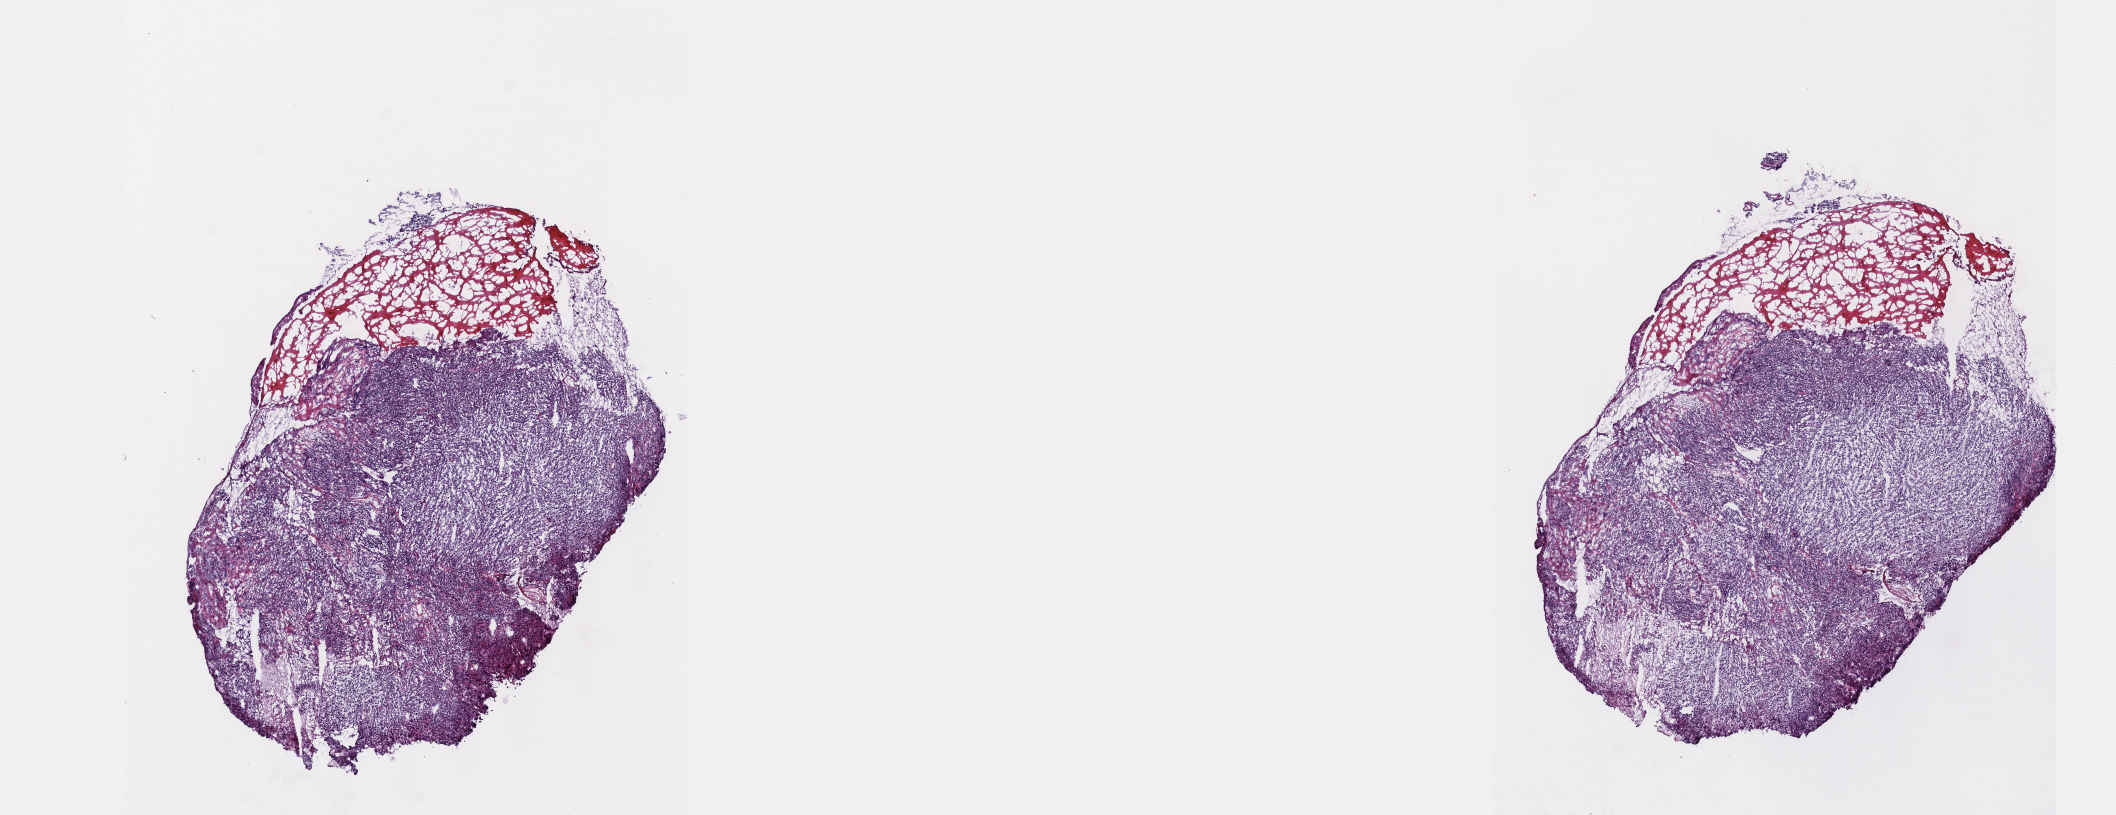
Digitized H&E tissue section (whole slide) — whole scanned area (about 17.1 x 6.6 mm) shown as a low-resolution overview, frozen section from the top of the tissue portion, cervix, primary tumour sample. Patient: female, age at initial diagnosis 72 years. Histologic grade: G3 (poorly differentiated). Composition of this section per pathologist review: tumour cells 80%, tumour nuclei 80%, normal cells 0%, stromal cells 20%, necrosis 0%. Infiltration values recorded for this section: lymphocyte infiltration 40%, monocyte infiltration 20%, neutrophil infiltration 20%.
- histologic diagnosis: Mucinous adenocarcinoma, endocervical type (cervix uteri)
- FIGO stage: IB